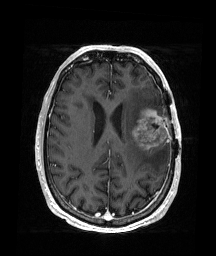
Brain MRI from a brain-tumour surgery series, one axial slice. Position 71 of 176 along the scan axis. T1-weighted post-contrast. 216 × 256 image matrix. Case-level facts recorded for this patient, not image findings: histopathology: Glioblastoma; WHO grade: 4; IDH mutation: no.
Outlined on this slice (manually delineated by an expert):
- tumour: box from (x=132, y=108) to (x=168, y=152) px